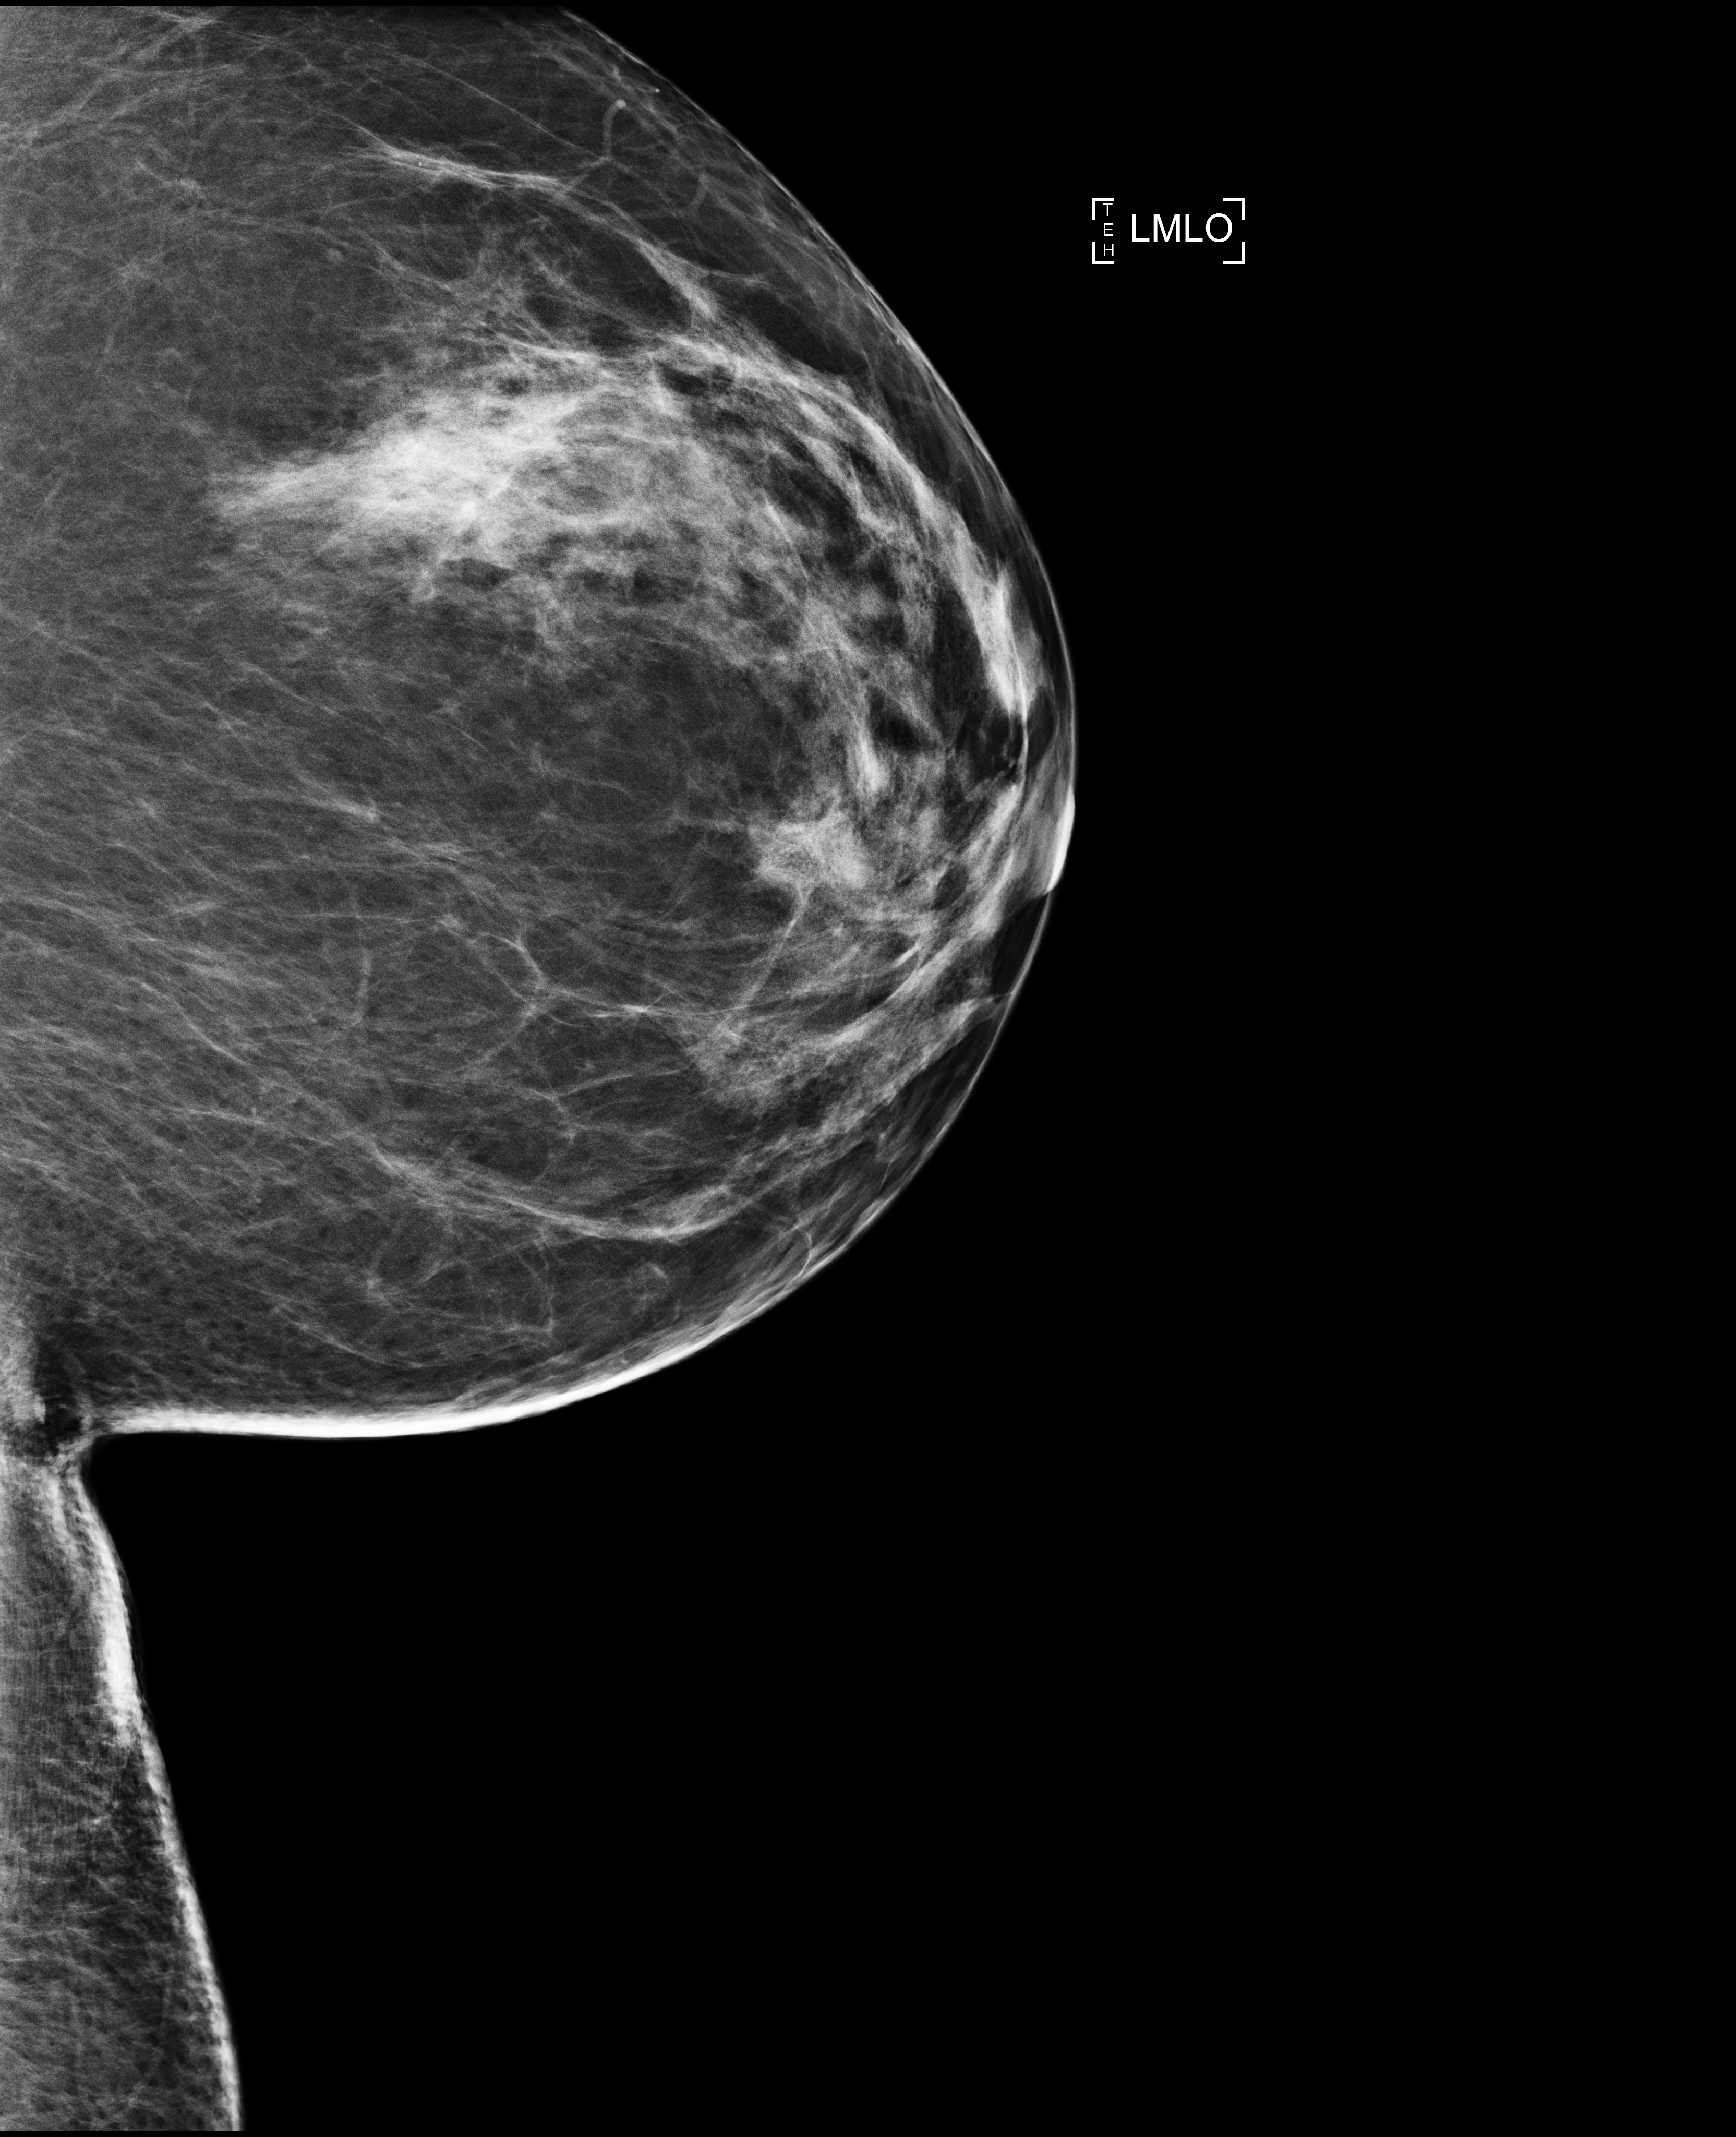
Annual screening mammography examination, compressed breast thickness 79 mm. Patient aged 65 years (female).
Image type: full-field digital mammogram. Breast: left. Projection: medio-lateral oblique projection.